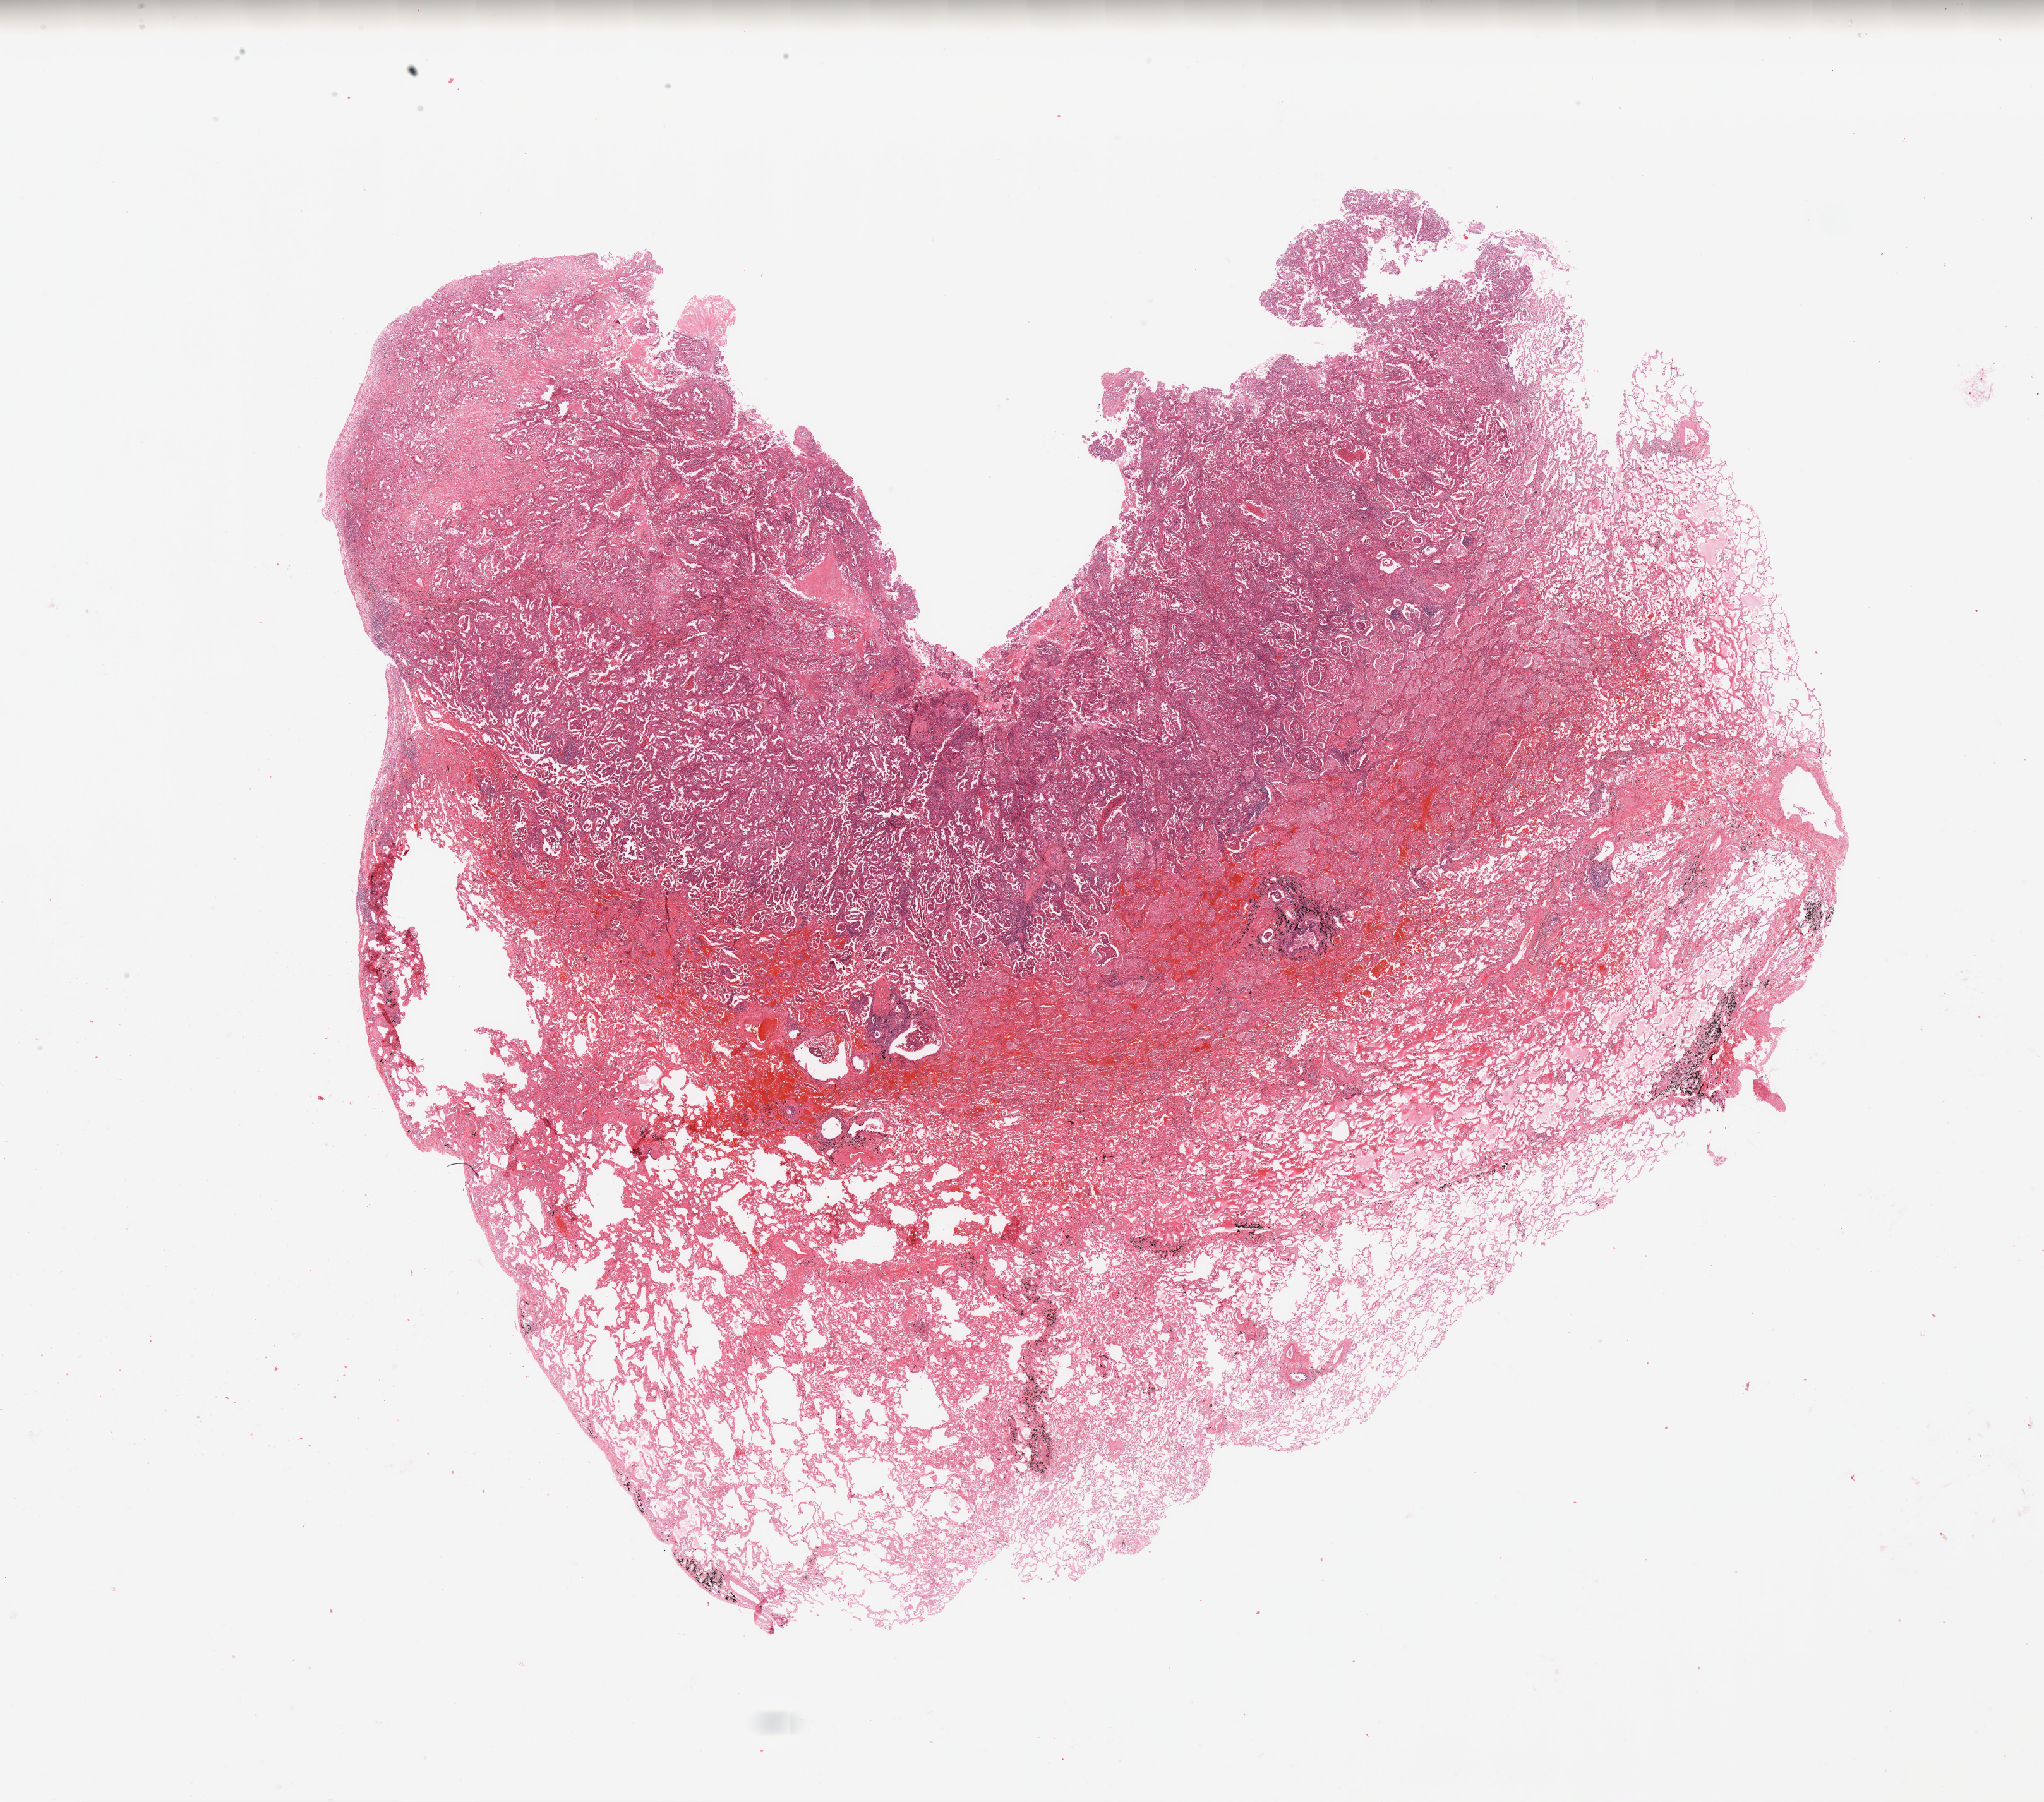
Whole-slide histology image, H&E — a low-resolution overview of the entire scanned area, about 25.6 x 22.6 mm, lung, tumour tissue. Patient: female, age 67 years. Histologic grade: G2 (moderately differentiated).
AJCC pathologic stage: IIIA. Diagnosis: Adenocarcinoma, NOS.